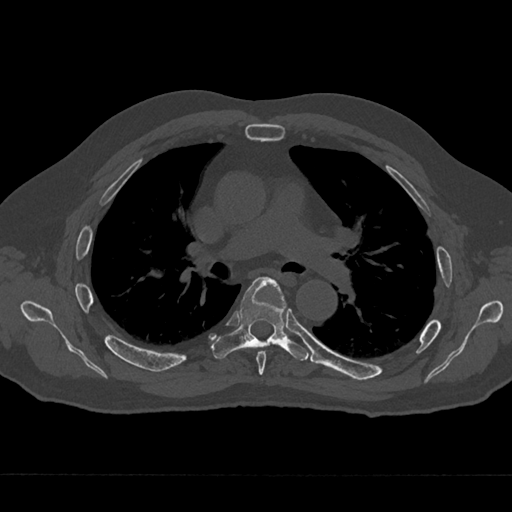
CT including the spine, one axial slice; slice 441 of 797 in the series (ordered by position); reconstruction kernel Br40s/3; bone window (W 1800 / L 400 HU); 0.5 mm slice thickness; 512 × 512 image matrix. Patient: male, 75 years. From the clinical record (not read from this slice): primary cancer: renal; vertebrae with lytic lesions (as recorded): T4.
Outlined on this slice (semi-automatically segmented with operator editing):
- T5 vertebra: bounding box <256,351,266,375> (left, top, right, bottom; pixels)
- T6 vertebra: <212,277,309,361>